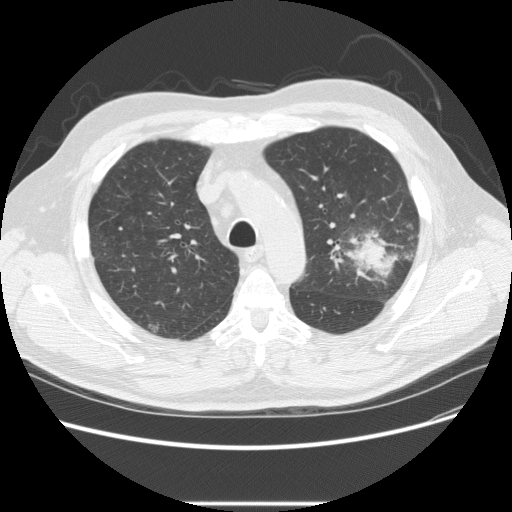
Low-dose screening chest CT, one axial slice; slice 167 of 233 in the series (ordered by position); 120 kVp; lung window (W 1500 / L -600 HU); 512 × 512 image matrix, field of view 380 × 380 mm.
Annotated regions visible in this slice (manually delineated by an expert):
- lesion 1 (tumor, upper lobe of left lung): bounding box [x1, y1, x2, y2] px = [352, 236, 399, 283]